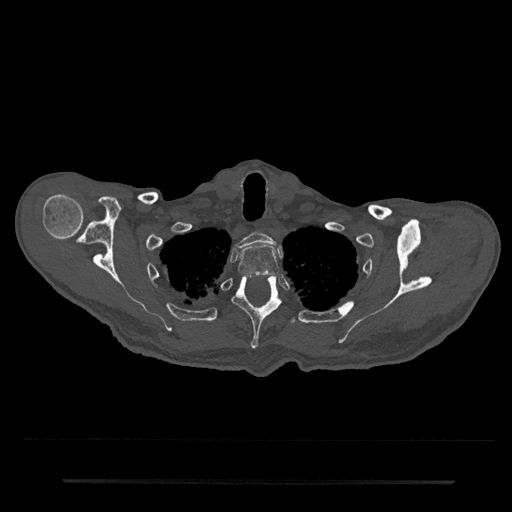
CT including the spine, one axial slice; position 668 of 797 along the scan axis; reconstruction kernel Br40s/3; bone window (W 1800 / L 400 HU); 0.5 mm slice thickness; 512 × 512 image matrix. Patient: male, 74 years. Case-level facts recorded for this patient, not image findings: primary cancer: prostate.
Structures marked on this image (semi-automatically segmented with operator editing):
- T1 vertebra: bounding box <236,232,276,249> (left, top, right, bottom; pixels)
- T2 vertebra: <237,244,280,276>
- T3 vertebra: <232,275,282,349>
- T4 vertebra: <288,316,296,325>